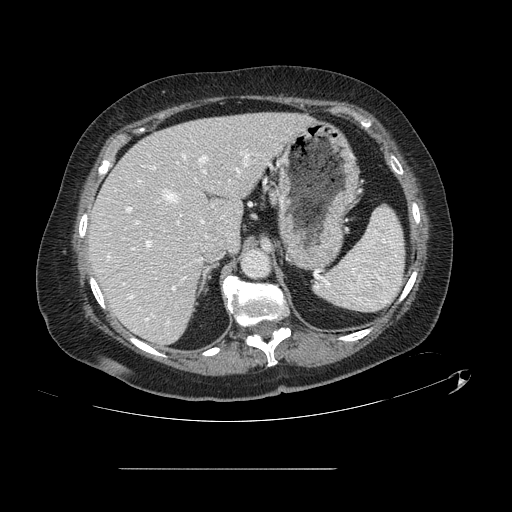
Contrast-enhanced abdominal CT, one axial slice. Position 91 of 148 along the scan axis. 120 kVp. Soft-tissue window (W 400 / L 40 HU). 2.5 mm slice thickness. 512 × 512 image matrix. Female patient, age 75 years. Case-level facts recorded for this patient, not image findings: diagnosis: colorectal cancer liver metastases, imaged before liver resection.
Structures marked on this image (outlined manually by an expert reader):
- hepatic veins: bounding box <130,155,240,320> (left, top, right, bottom; pixels)
- liver: <90,114,308,344>
- planned liver remnant (the part of the liver to remain after resection): <90,114,308,344>
- portal vein (with intrahepatic branches): <127,151,251,290>